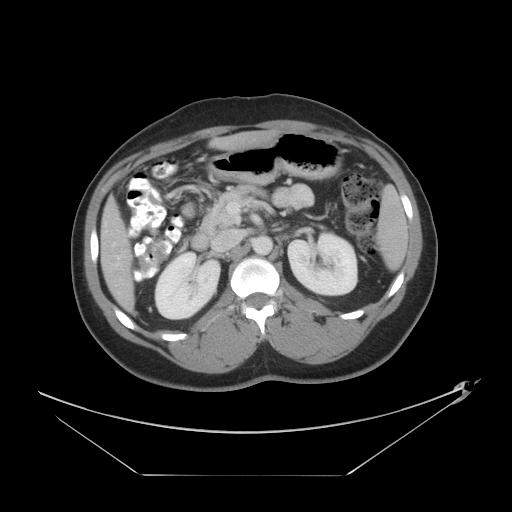
Contrast-enhanced abdominal CT, one axial slice; position 20 of 44 along the scan axis; 120 kVp; intravenous contrast given; soft-tissue window (W 400 / L 40 HU); 512 × 512 image matrix. Male patient, age 49 years. From the clinical record (not read from this slice): diagnosis: colorectal cancer liver metastases, imaged before liver resection; multiple liver metastases: no; largest metastasis: 8.5 cm; chemotherapy before resection: yes.
Outlined on this slice (outlined manually by an expert reader):
- hepatic veins: bounding box [x1, y1, x2, y2] px = [117, 232, 136, 278]
- liver: [101, 131, 278, 313]
- planned liver remnant (the part of the liver to remain after resection): [214, 131, 278, 151]